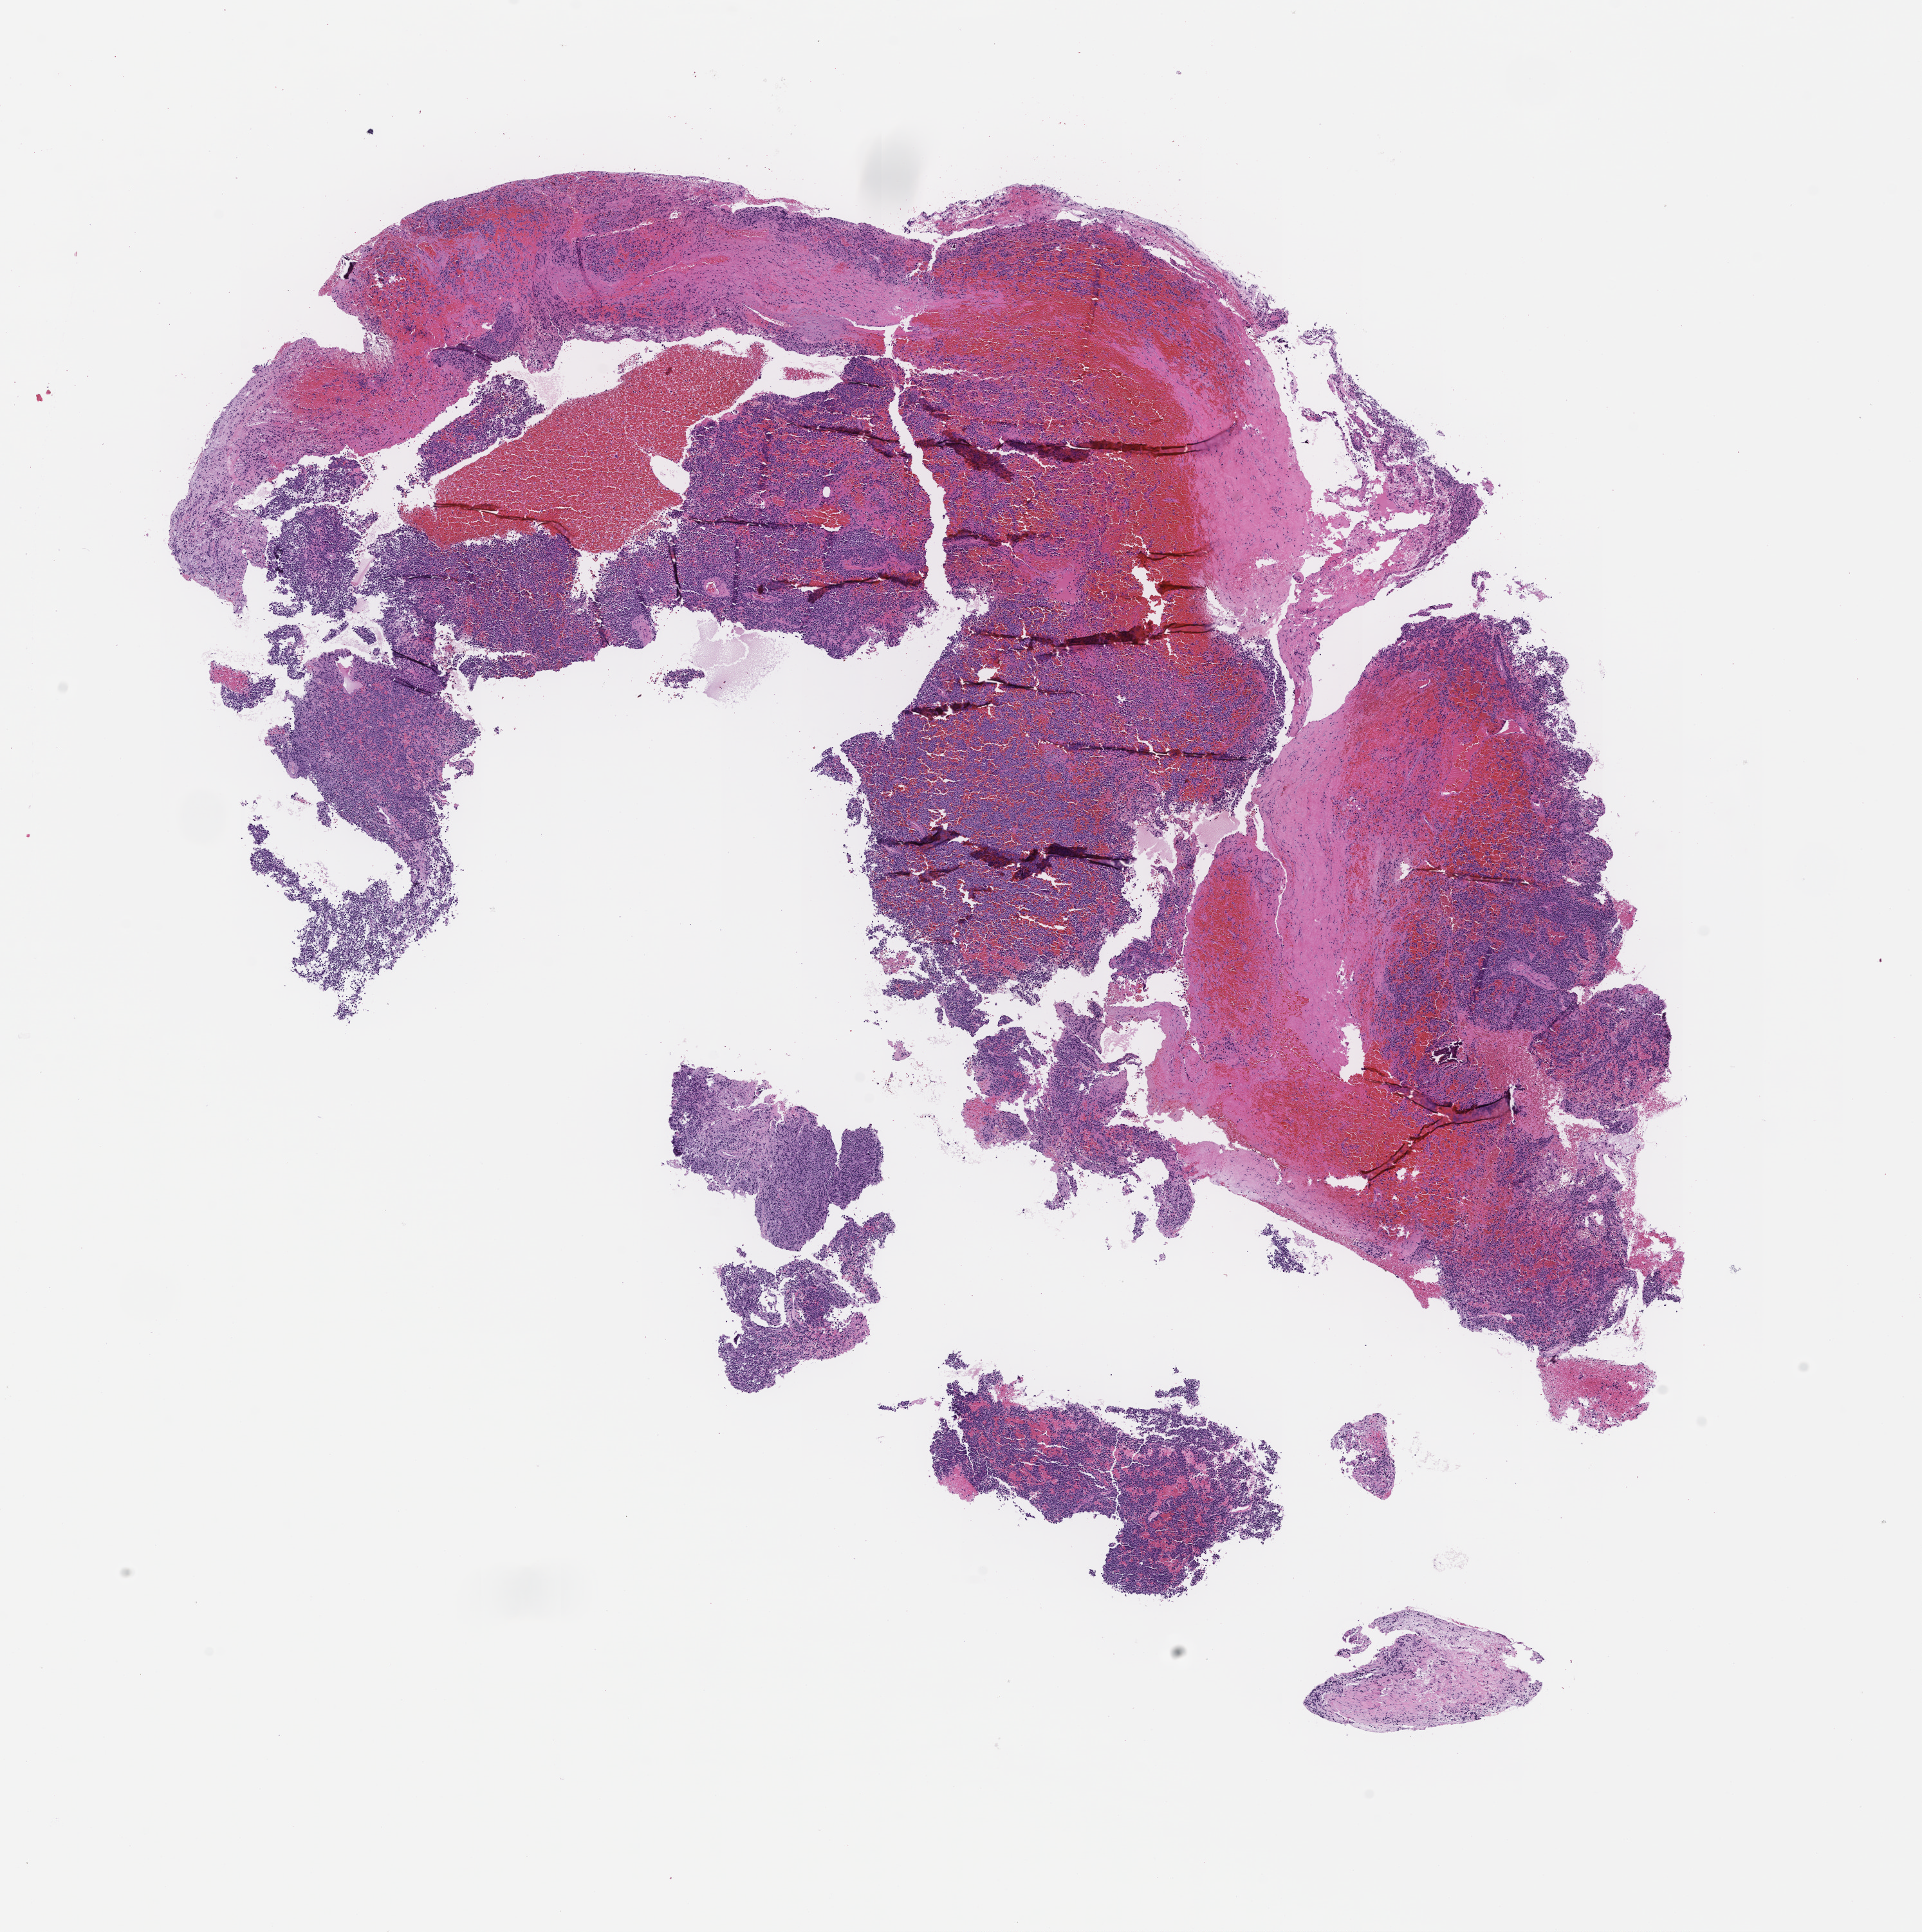
Digitized H&E-stained section, low-resolution overview of the scanned area, about 12.1 x 12.1 mm, FFPE section, collected at disease progression. Patient sex: male.
- this section: metastasis (sampled organ not recorded)
- patient diagnosis (primary): Plasma Cell Myeloma